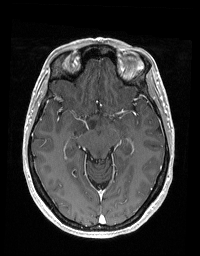
Brain MRI from a brain-tumour surgery series, one axial slice. Slice 111 of 192 in the series (ordered by position). T1-weighted post-contrast. 1 mm slice thickness. 200 × 256 image matrix, field of view 195 × 250 mm. From the clinical record (not read from this slice): histopathology: Glioblastoma; WHO grade: 2; IDH mutation: no.
Structures marked on this image (manually delineated by an expert):
- tumour: bounding box <79,118,95,133> (left, top, right, bottom; pixels)